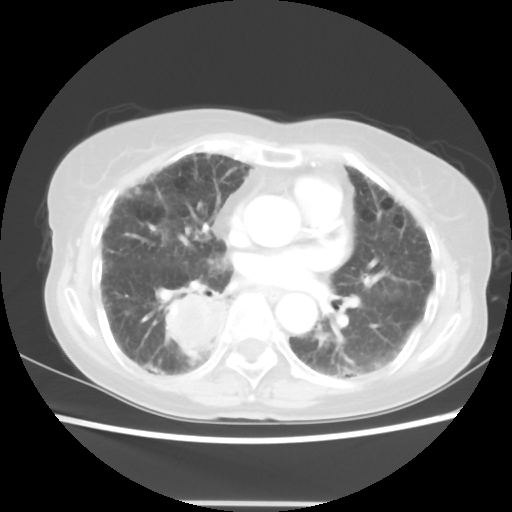
Chest CT, one axial slice. Lung window (W 1500 / L -600 HU). 5 mm slice thickness. 512 × 512 image matrix, field of view 325 × 325 mm. Female patient, age 71 years. From the clinical record (not read from this slice): clinical TNM (as recorded): T3 N0 M0.
Annotated regions visible in this slice (bounding box drawn by a radiologist):
- lung tumour (recorded histology: squamous cell carcinoma): bounding box [x1, y1, x2, y2] px = [159, 288, 231, 363]